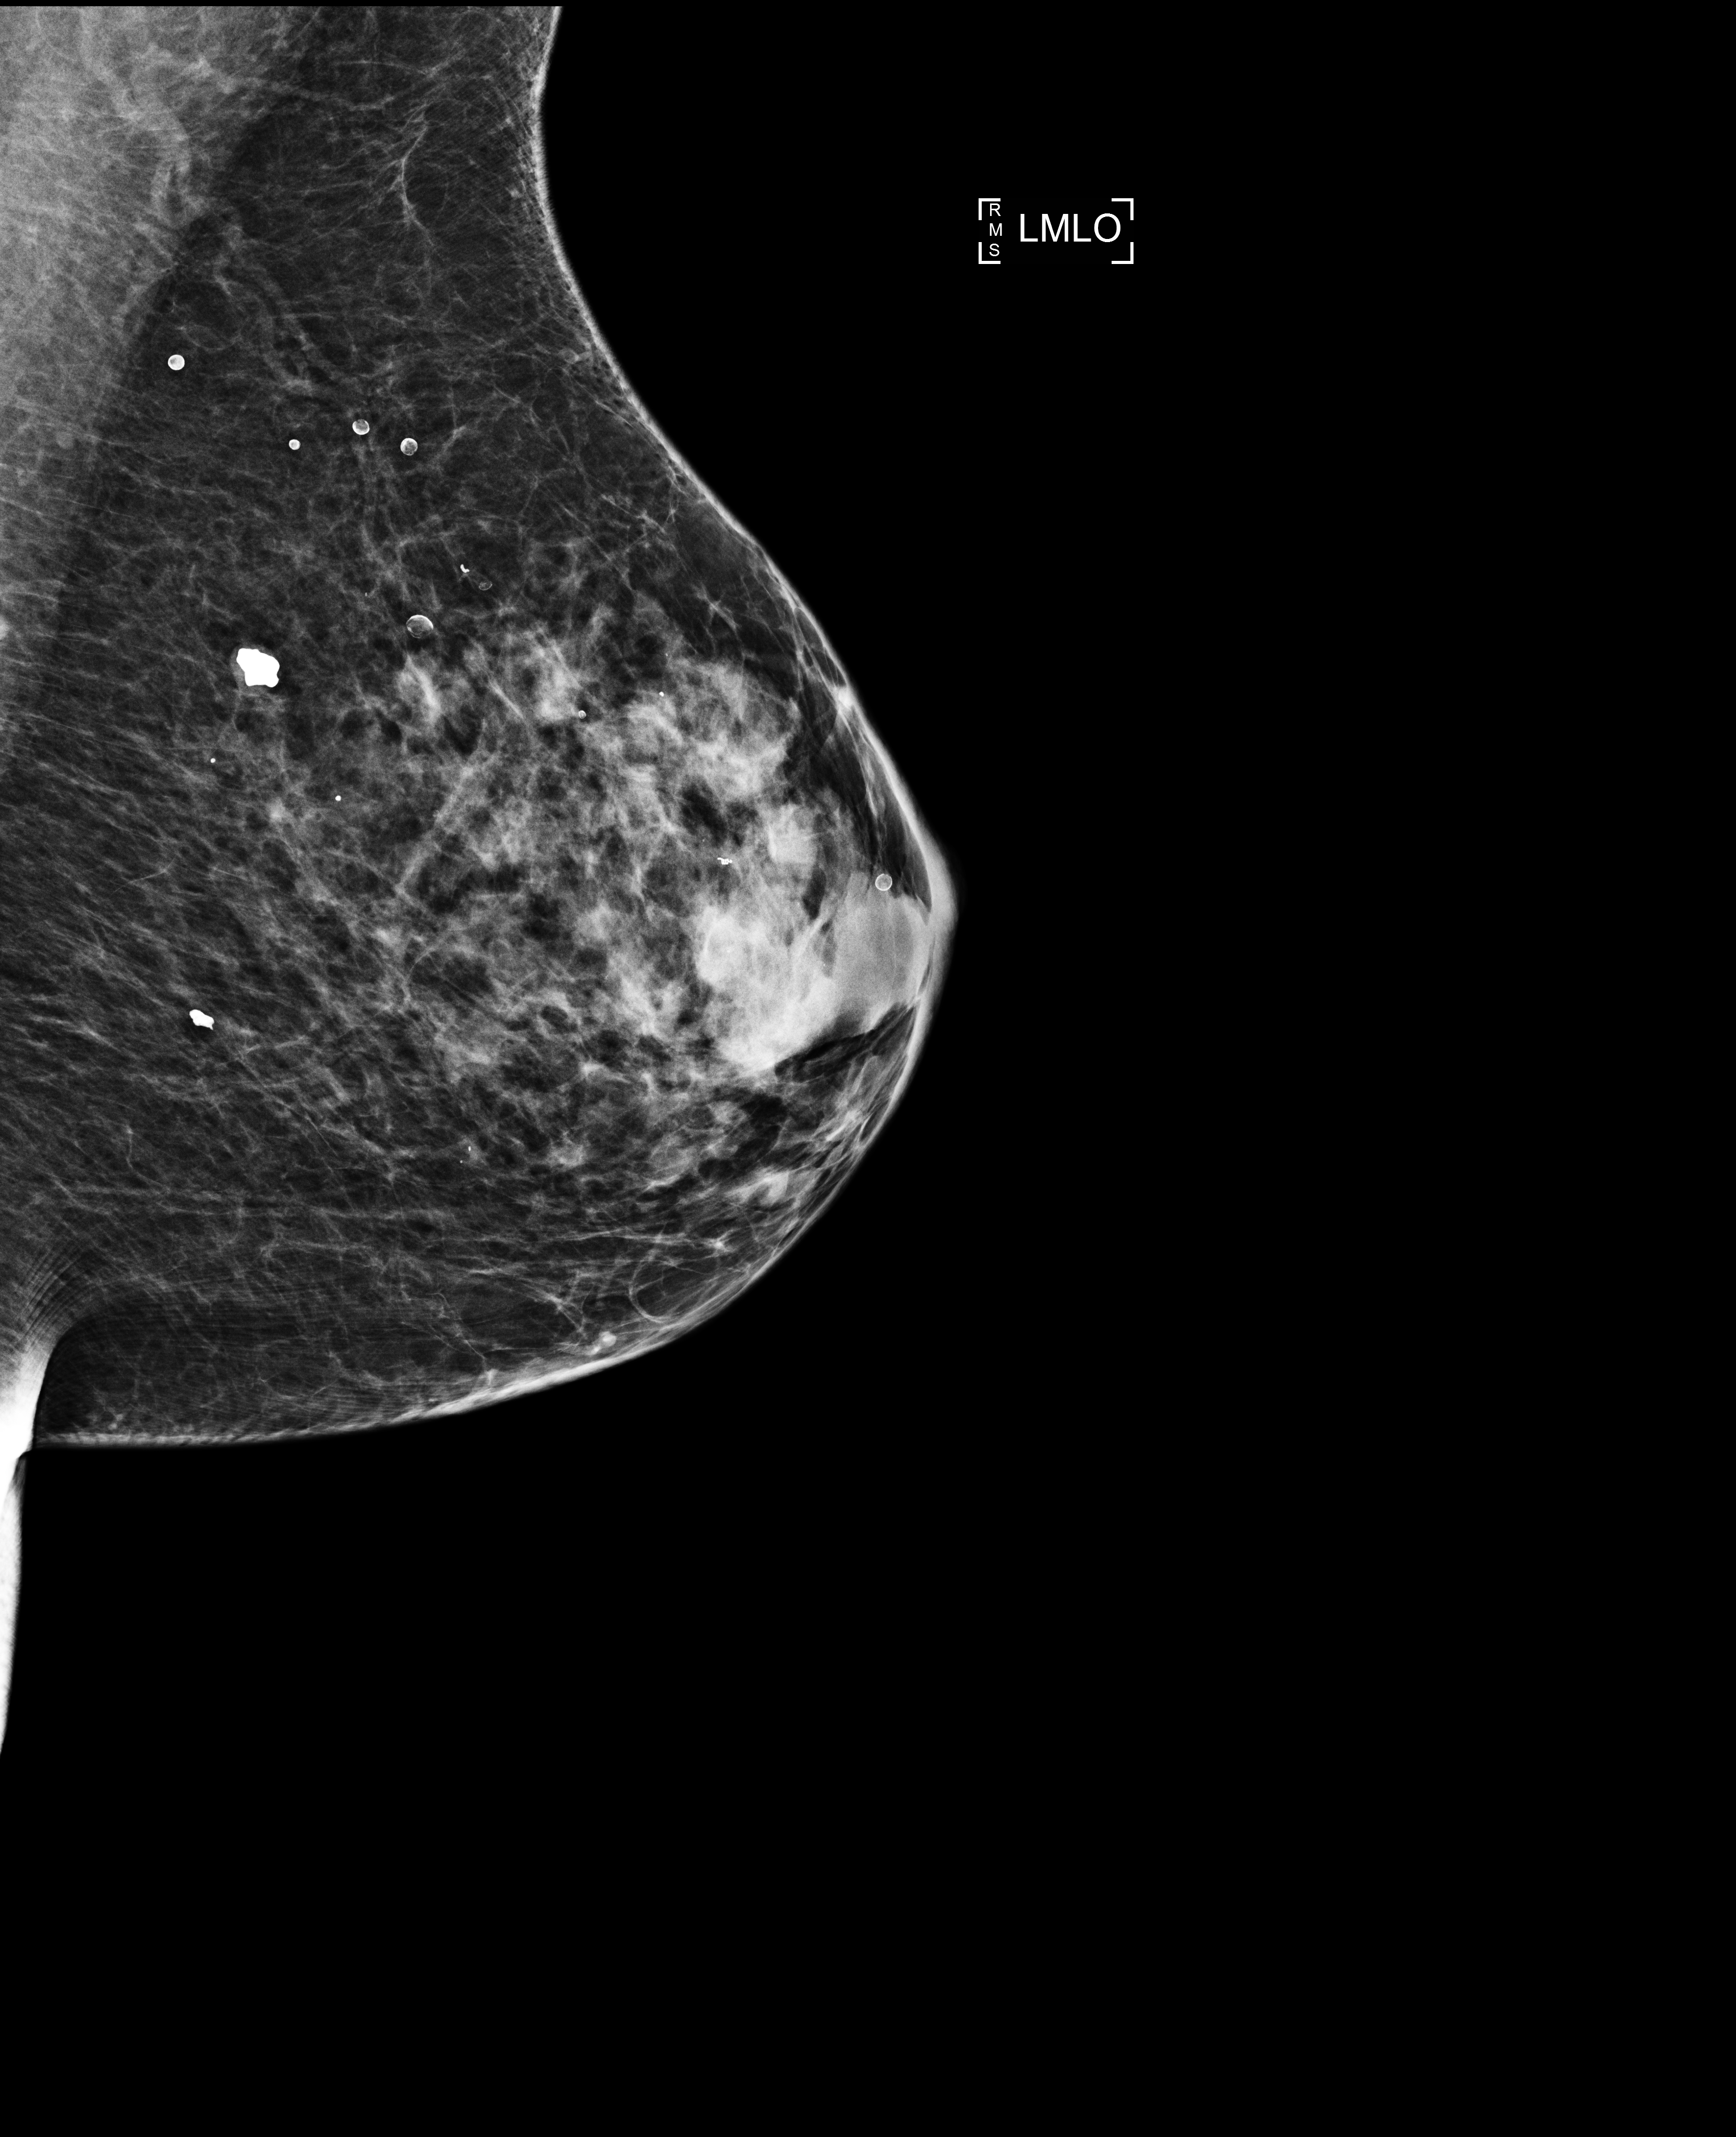
Screening examination; system: Selenia Dimensions. Patient: female, 68 years.
Image type: full-field digital mammogram. Breast: left. Projection: medio-lateral oblique projection.